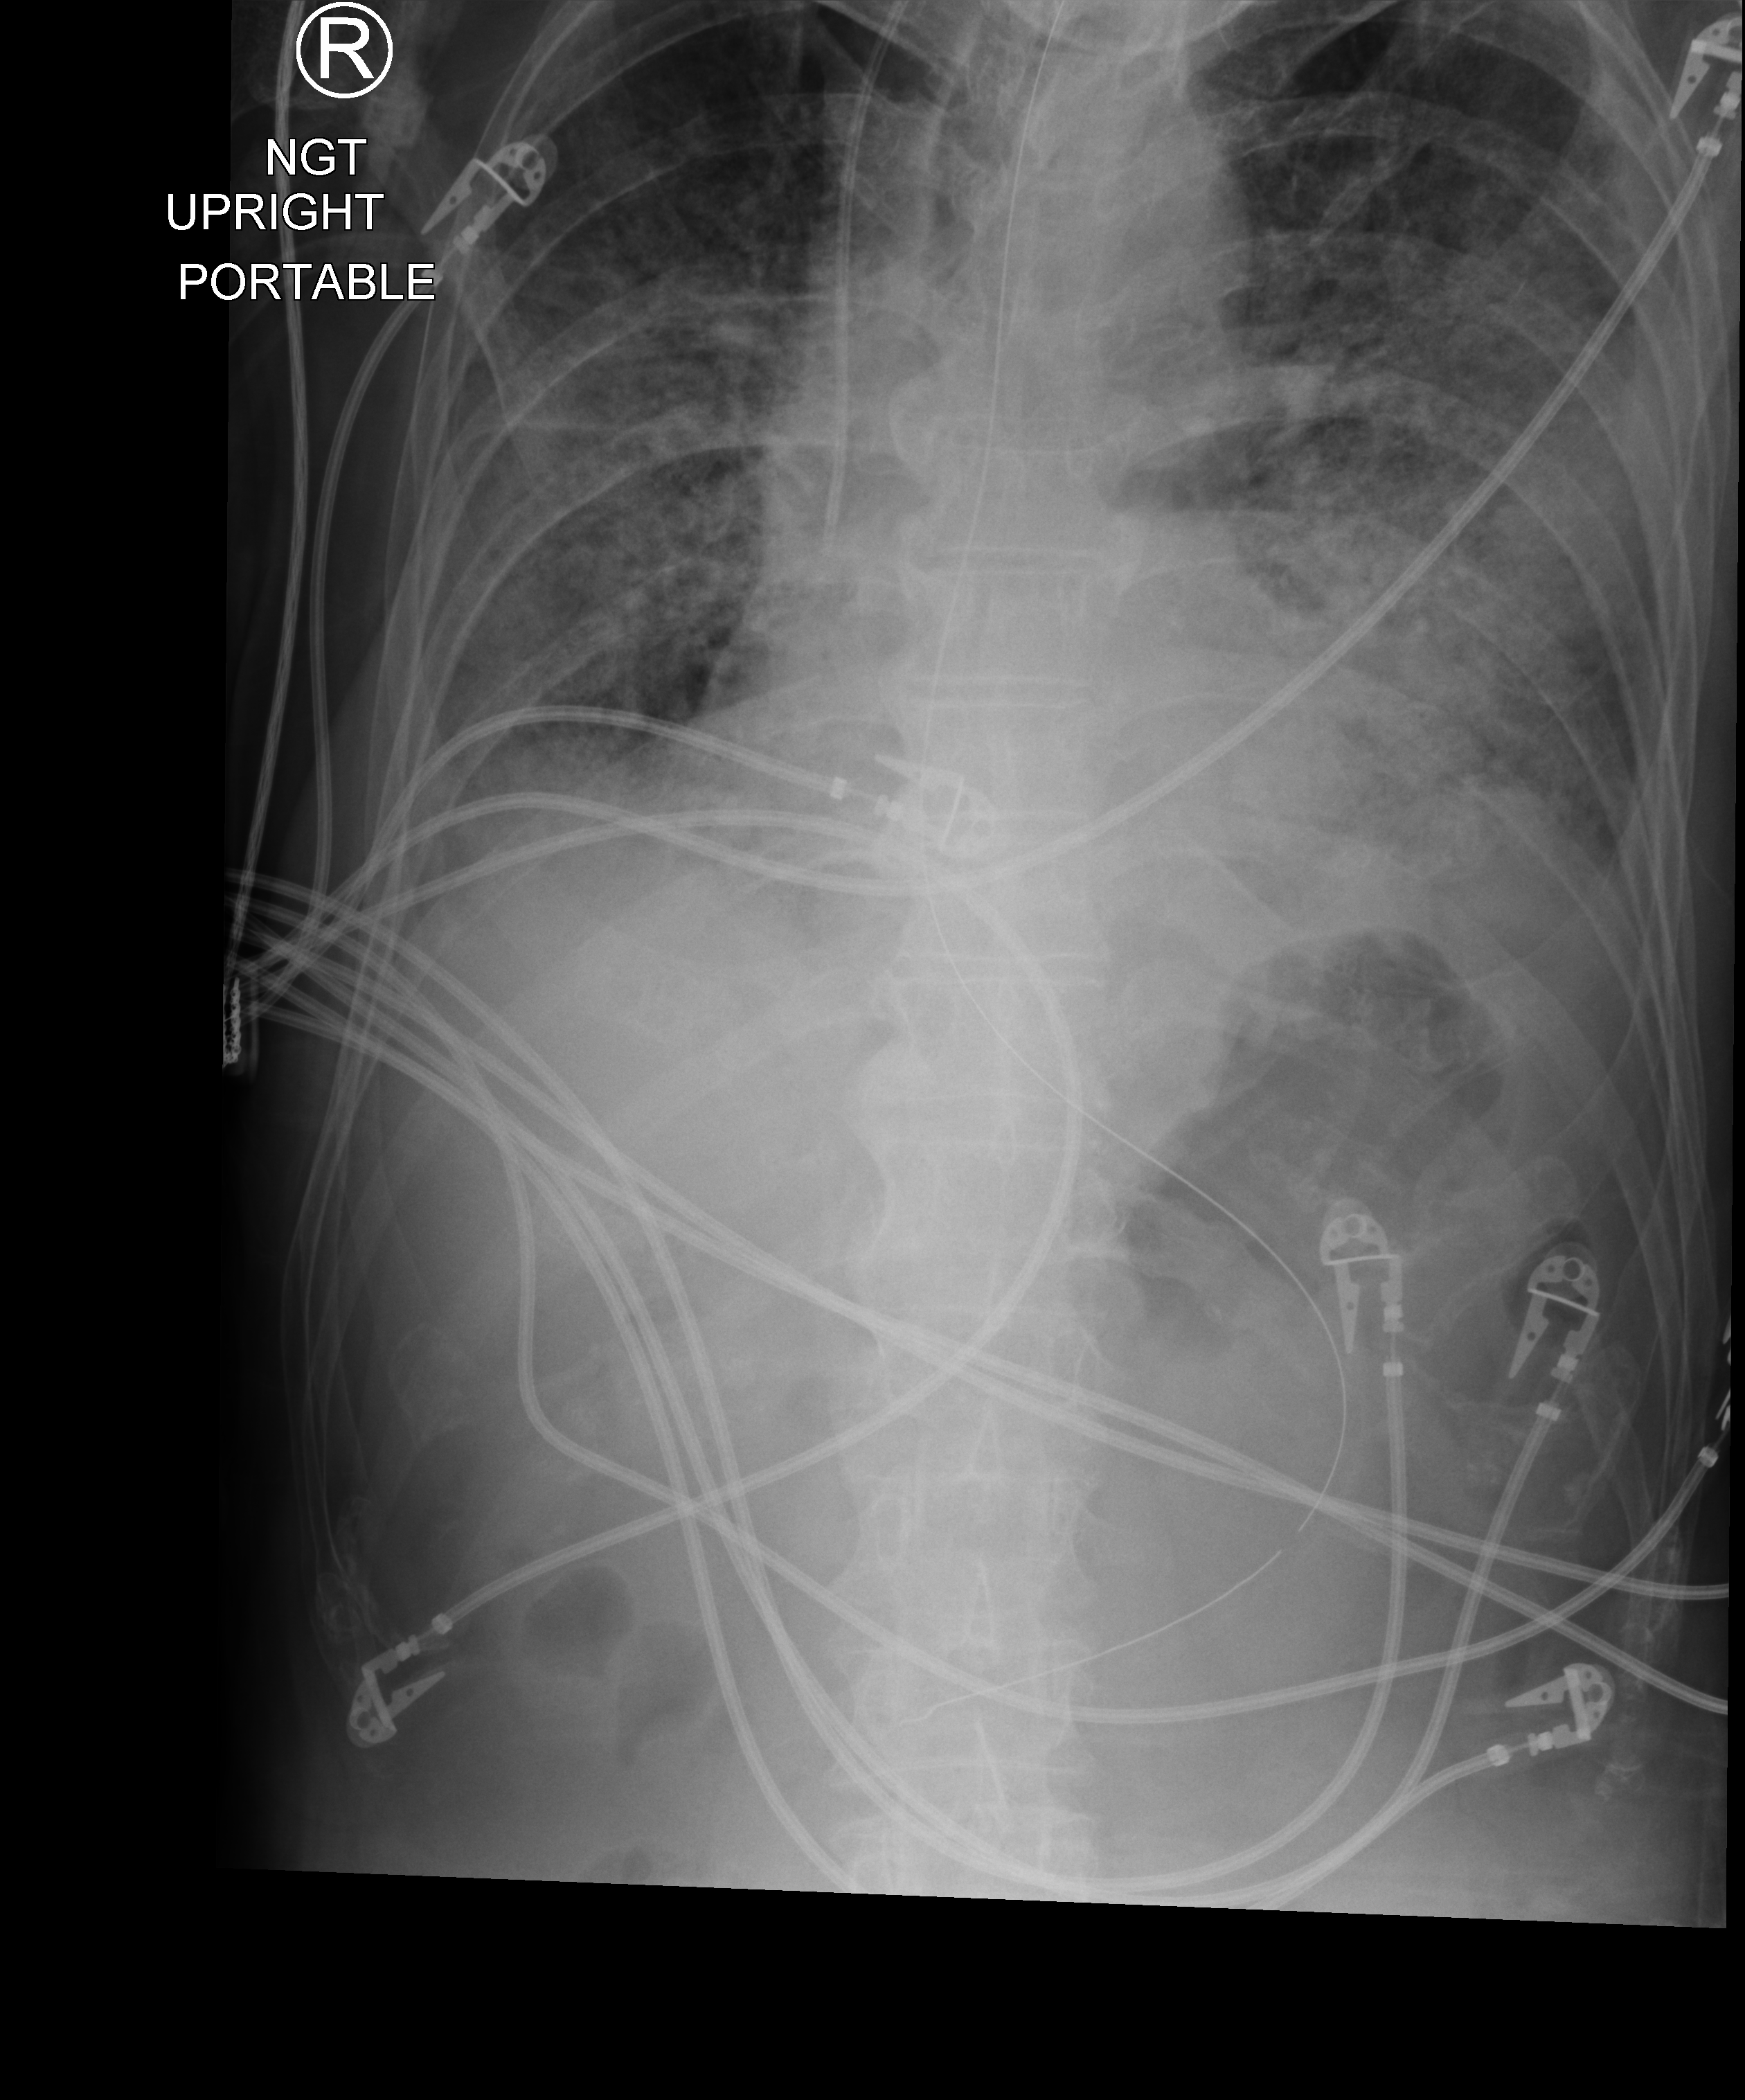
Portable chest radiograph; anteroposterior (AP) projection. Patient hospitalised with COVID-19; male, aged 60–74 years.
Hospital-stay facts (about this admission, not read from this image; timing relative to this image not recorded): admitted to intensive care during this hospital stay: yes.